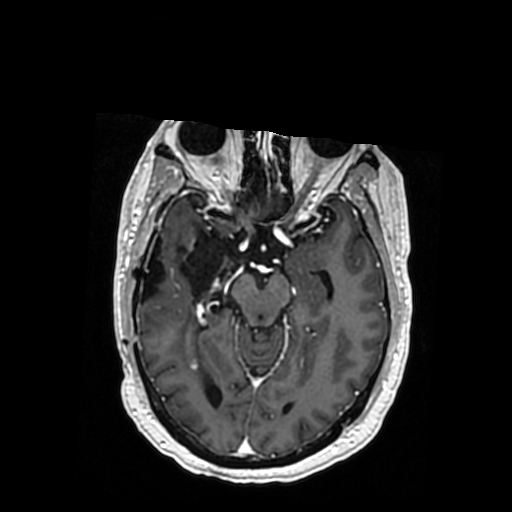
Brain MRI from a brain-tumour surgery series, one axial slice; slice 213 of 364 in the series (ordered by position); T1-weighted post-contrast; 0.5 mm slice thickness; 512 × 512 image matrix. Case-level facts recorded for this patient, not image findings: histopathology: Oligodendroglioma; WHO grade: 3; IDH mutation: yes; tumour location: Right Posterior Temporal Inferior Parietal.
Structures marked on this image (outlined manually by an expert reader):
- previous resection cavity: bounding box (x1, y1, x2, y2) in pixels: (141, 228, 239, 302)